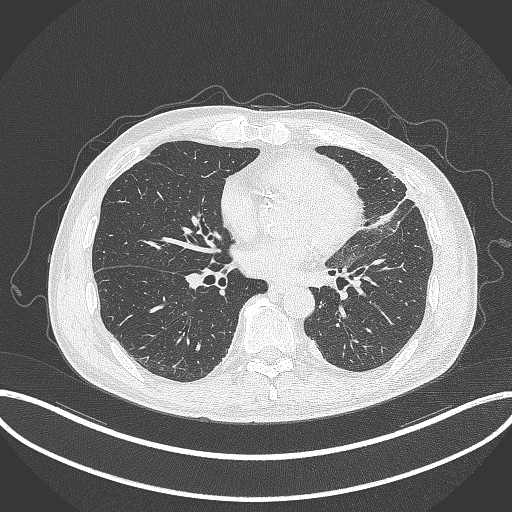
Chest CT, one axial slice; position 142 of 382 along the scan axis; reconstruction kernel B70f; 120 kVp; lung window (W 1500 / L -600 HU); 1 mm slice thickness; 512 × 512 image matrix, field of view 415 × 415 mm. Patient: male, 64 years. From the clinical record (not read from this slice): clinical TNM (as recorded): T4 N1 M0; histopathological grade: G3.
Structures marked on this image (rectangle marked by the reading radiologist):
- lung tumour (recorded histology: adenocarcinoma): box from (x=360, y=196) to (x=413, y=228) px